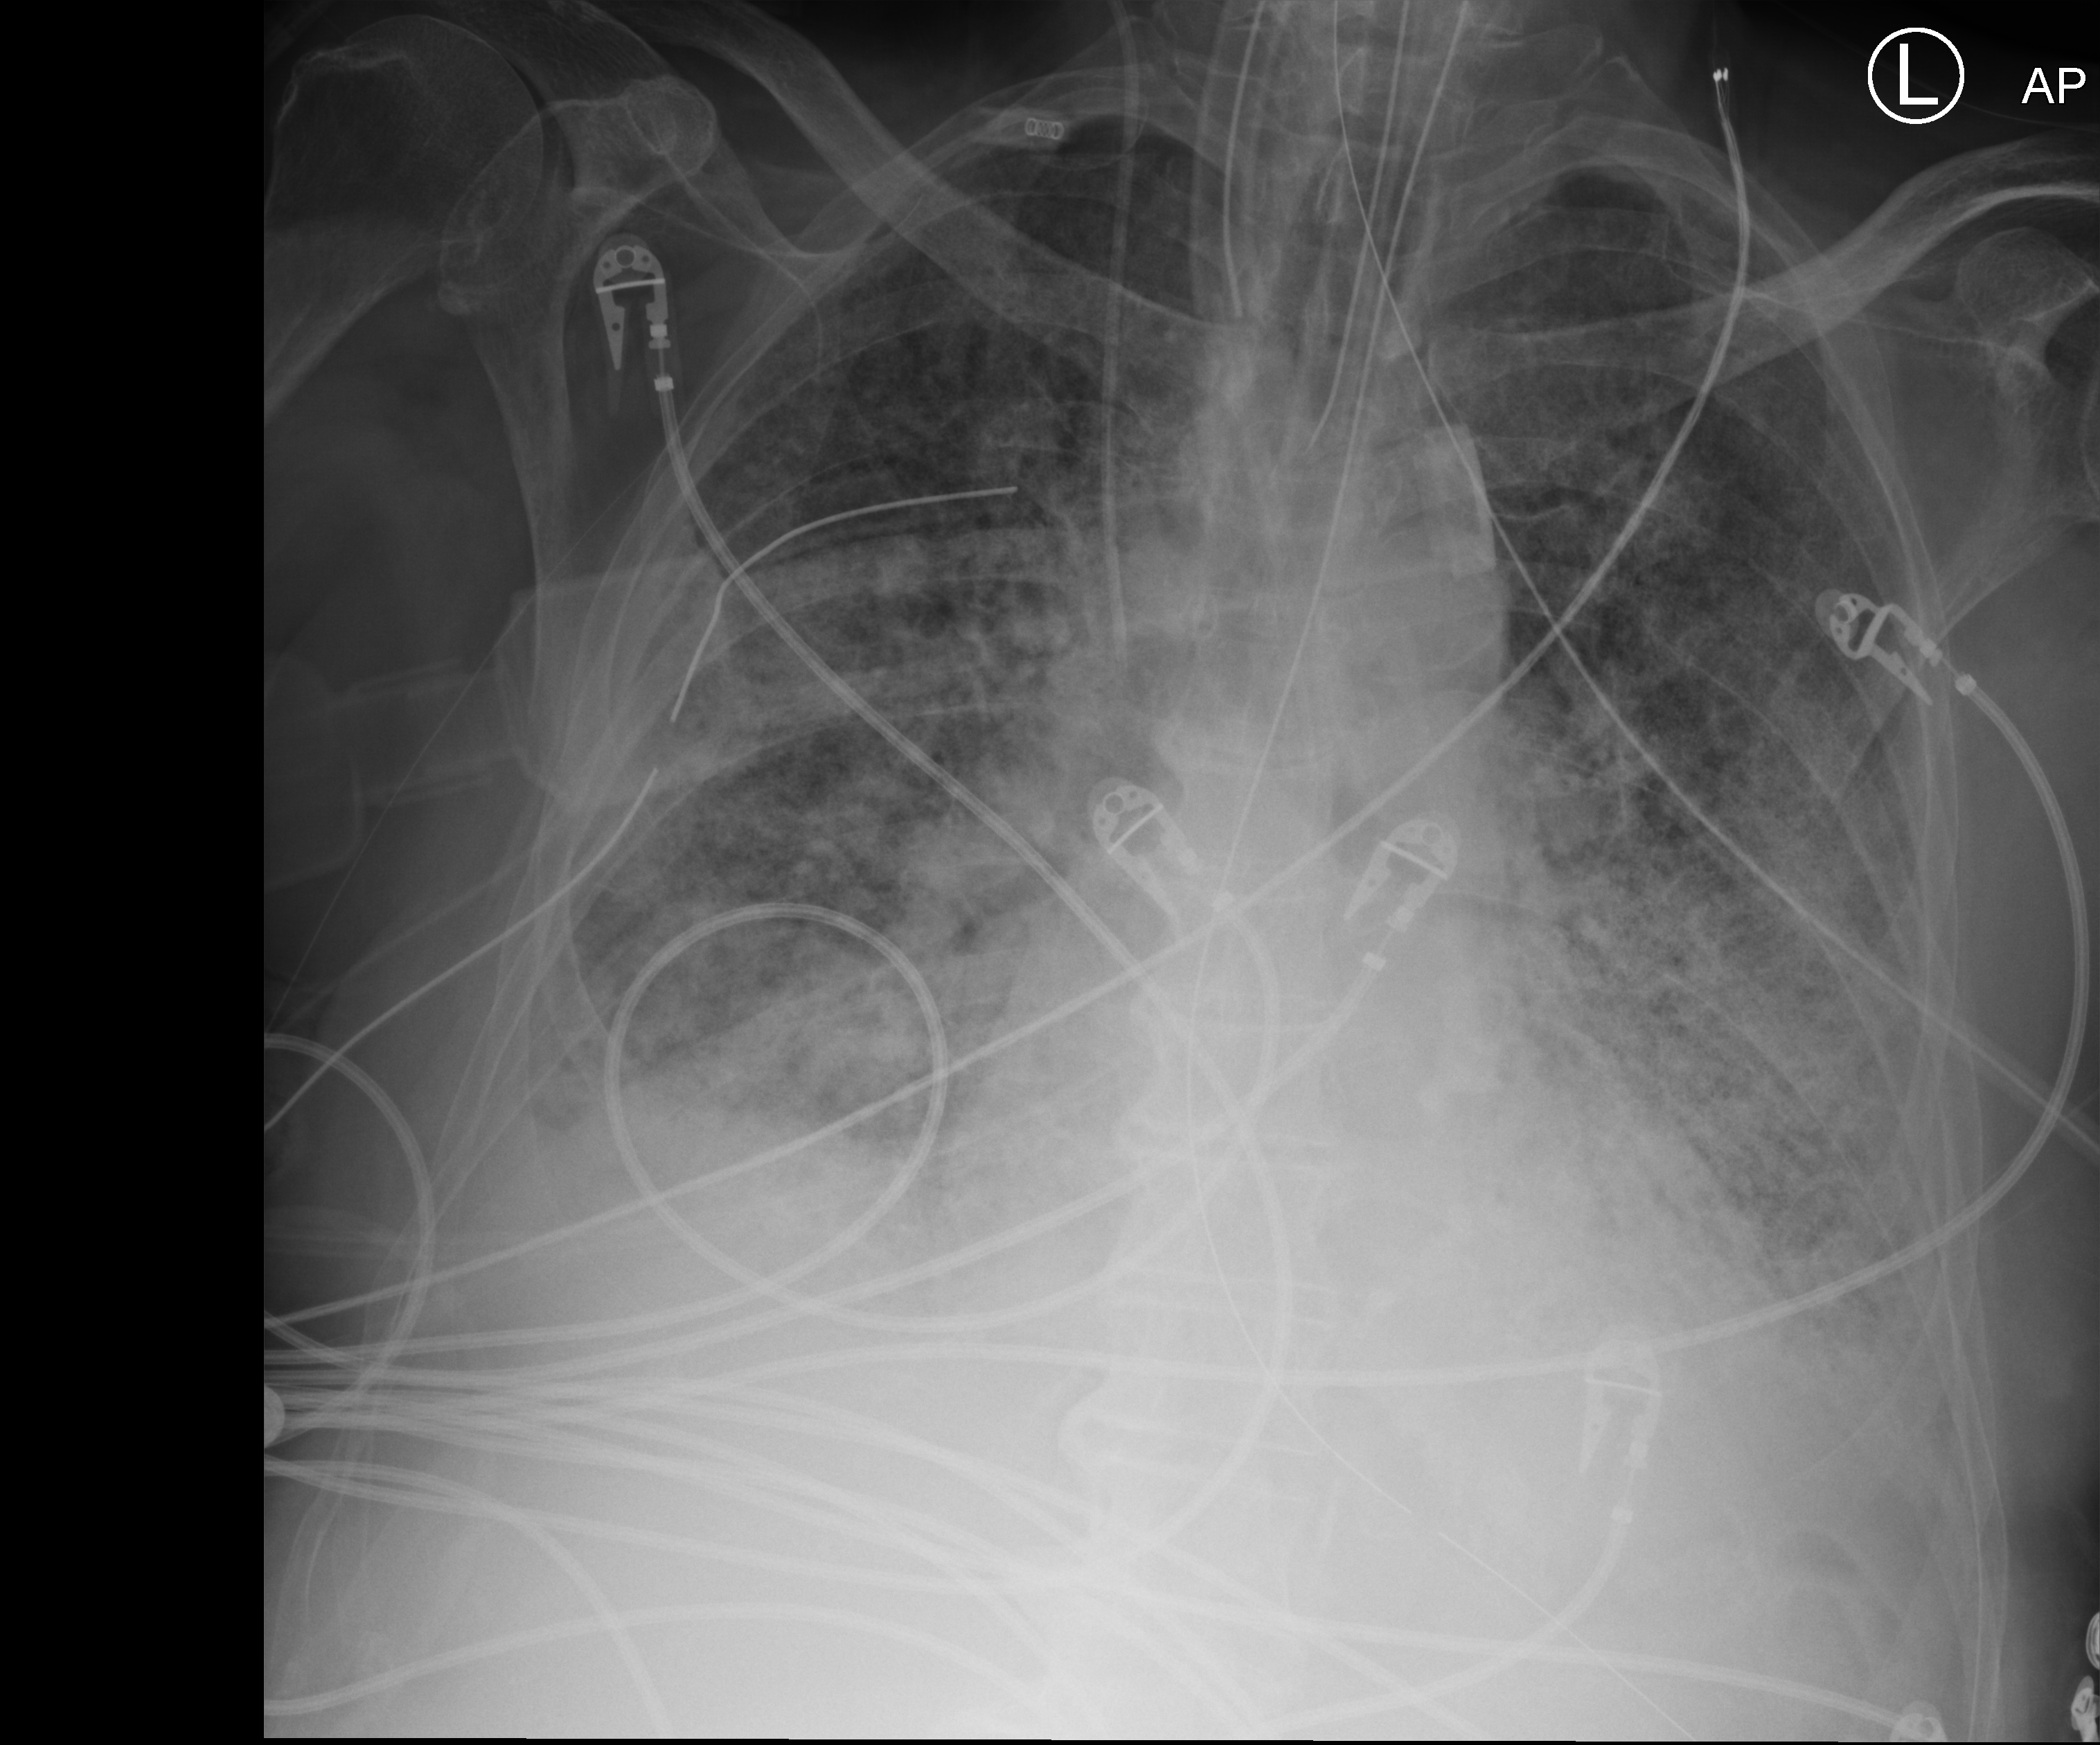
Chest X-ray (portable), anteroposterior (AP) projection. Patient hospitalised with COVID-19; male, aged 75–90 years.
Admission-level facts for this patient (not findings on this image; timing relative to this image not recorded):
- hypertension (admission record): no
- admitted to intensive care during this hospital stay: yes